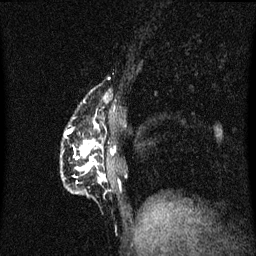
Breast MRI (dynamic contrast-enhanced), one sagittal slice; slice 15 of 60 in the series (ordered by position); dynamic contrast-enhanced series, image 2 of 3 at this slice position (ordered by acquisition); 1.5 T; TE 4.2 ms, TR 8.4 ms; 2 mm slice thickness; 256 × 256 image matrix, field of view 200 × 200 mm. Female patient, age 40 years.
Structures marked on this image (semi-automatic segmentation, software-assisted and operator-edited):
- analysis volume of interest (the breast-tissue region the enhancement analysis was run in; not a lesion): bounding box (x1, y1, x2, y2) in pixels: (61, 88, 111, 195)
- tumour enhancement mask (voxels above the 70 % enhancement threshold inside the analysis volume of interest): (65, 102, 106, 185)